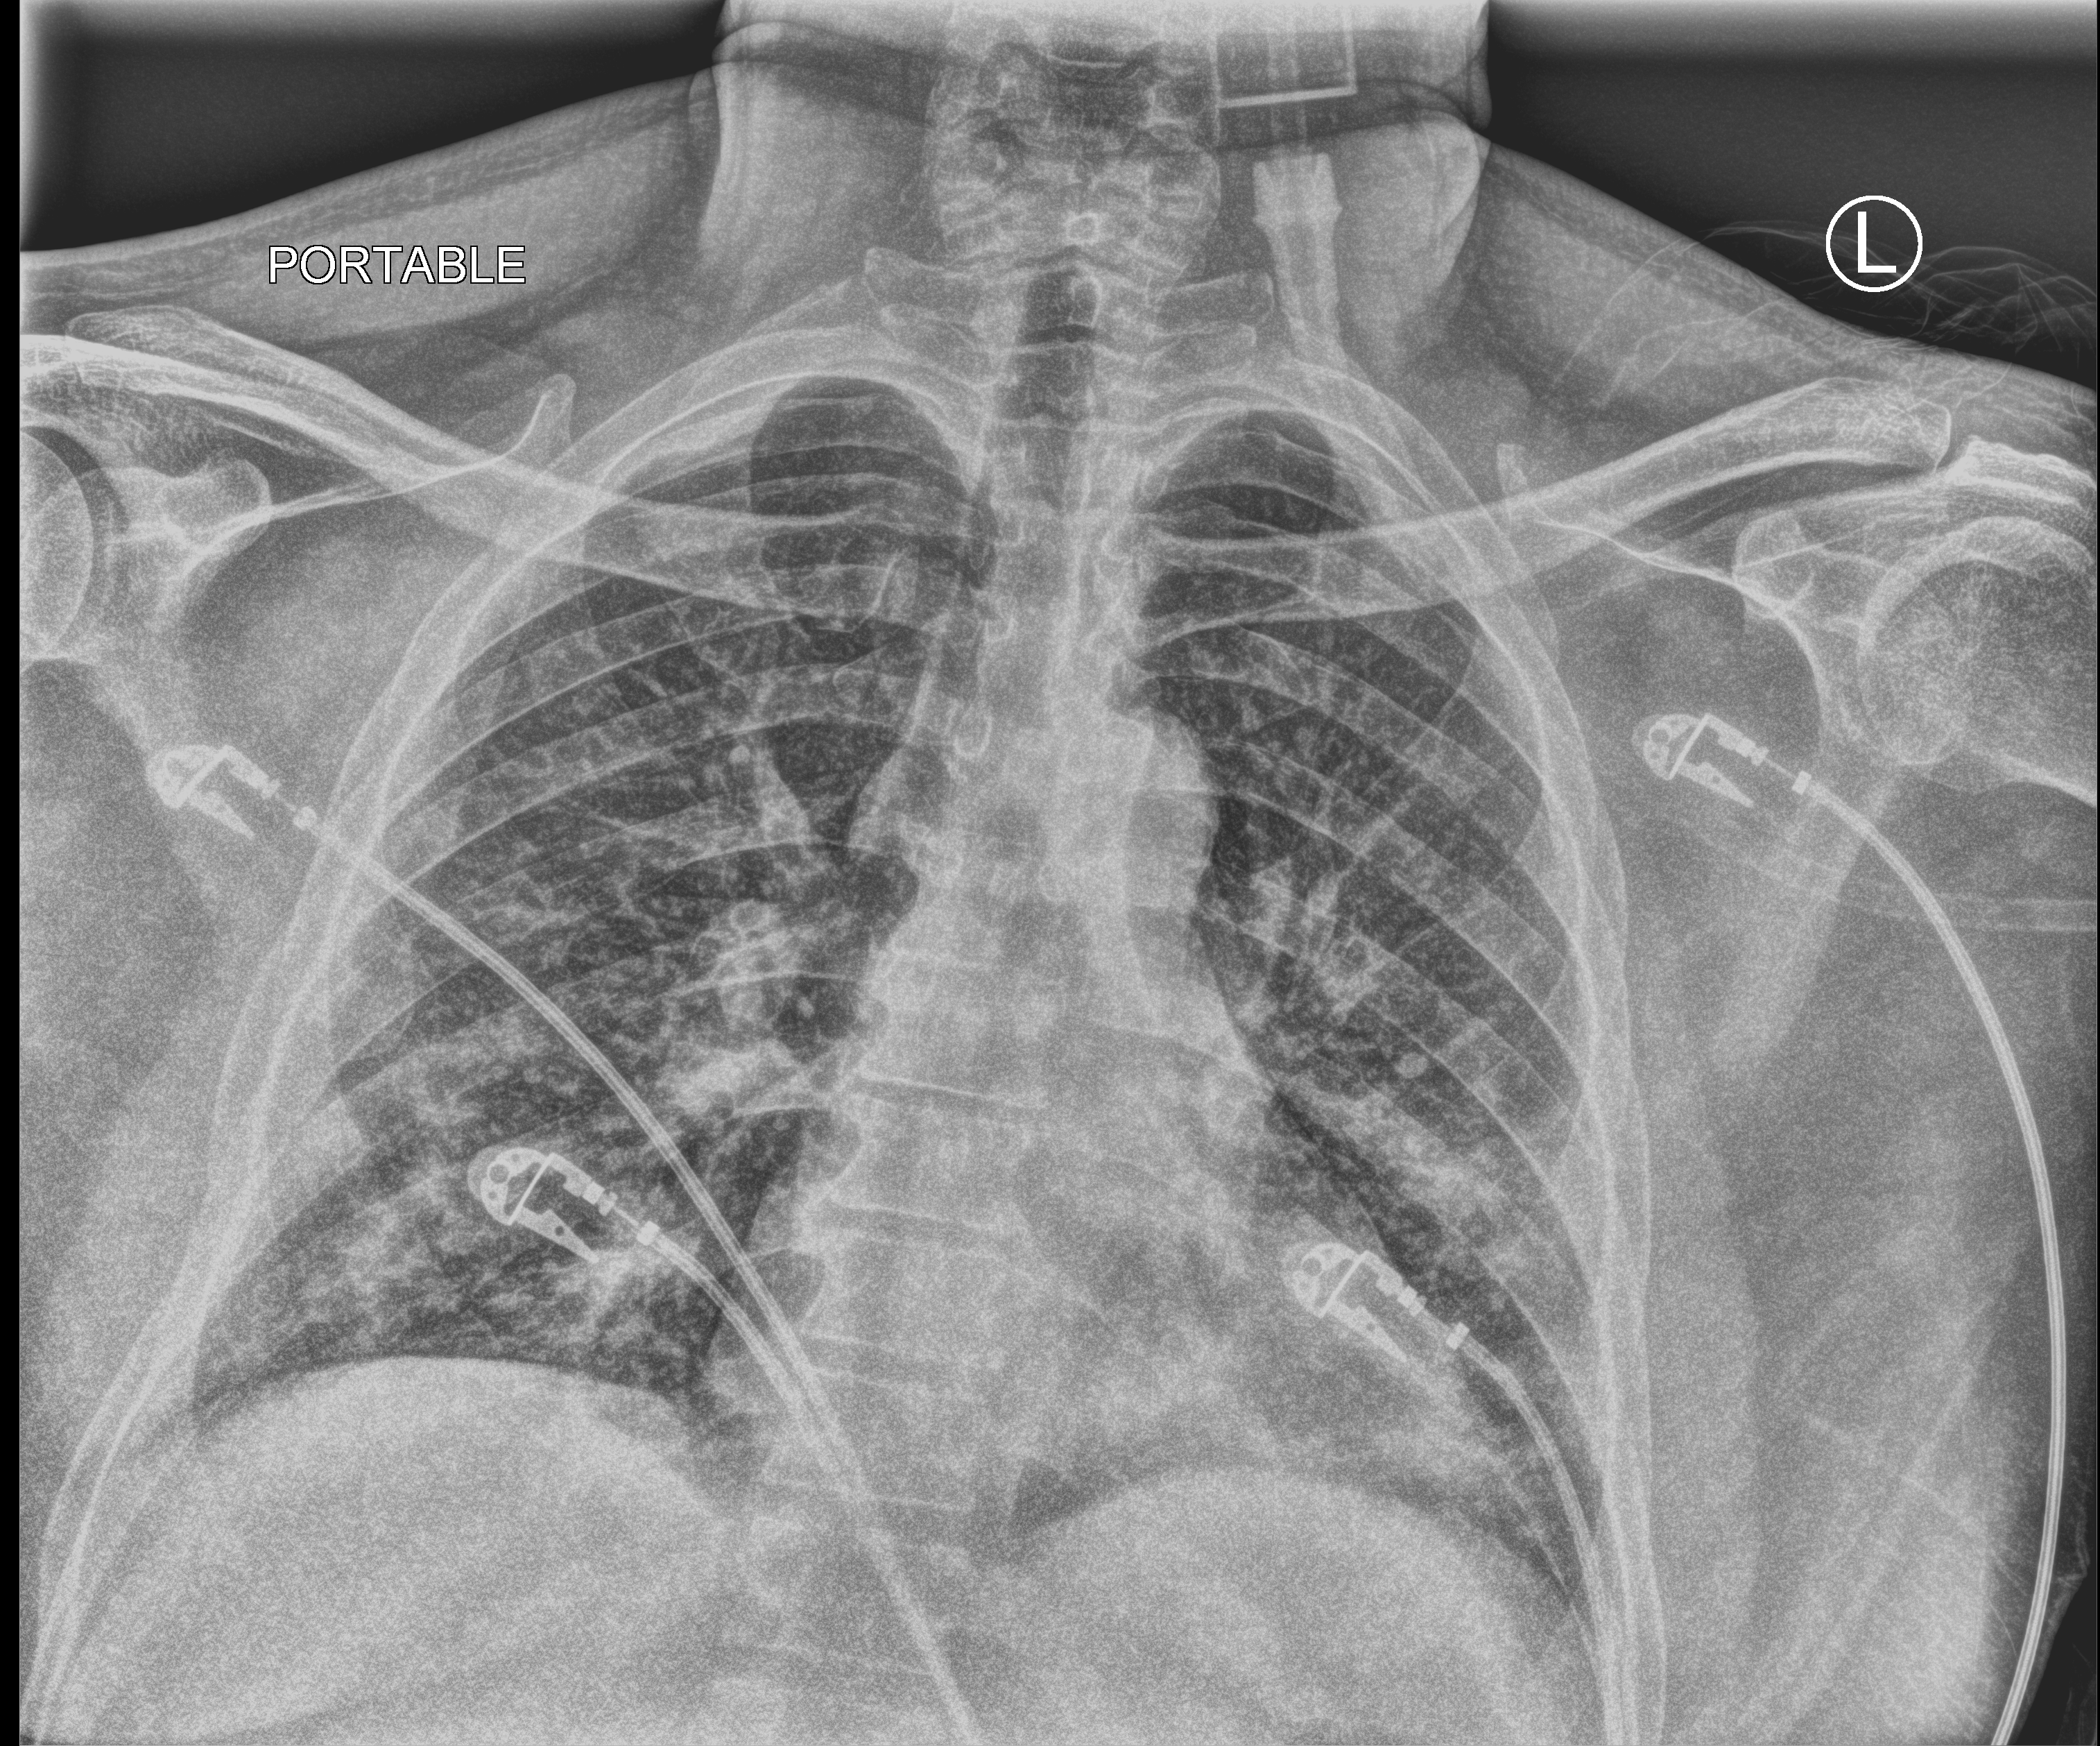
Chest X-ray (portable), anteroposterior (AP) projection. Patient hospitalised with COVID-19; male, aged 18–59 years.
Hospital-stay facts (about this admission, not read from this image; timing relative to this image not recorded): chronic kidney disease (admission record): no; mechanically ventilated during this hospital stay: yes.